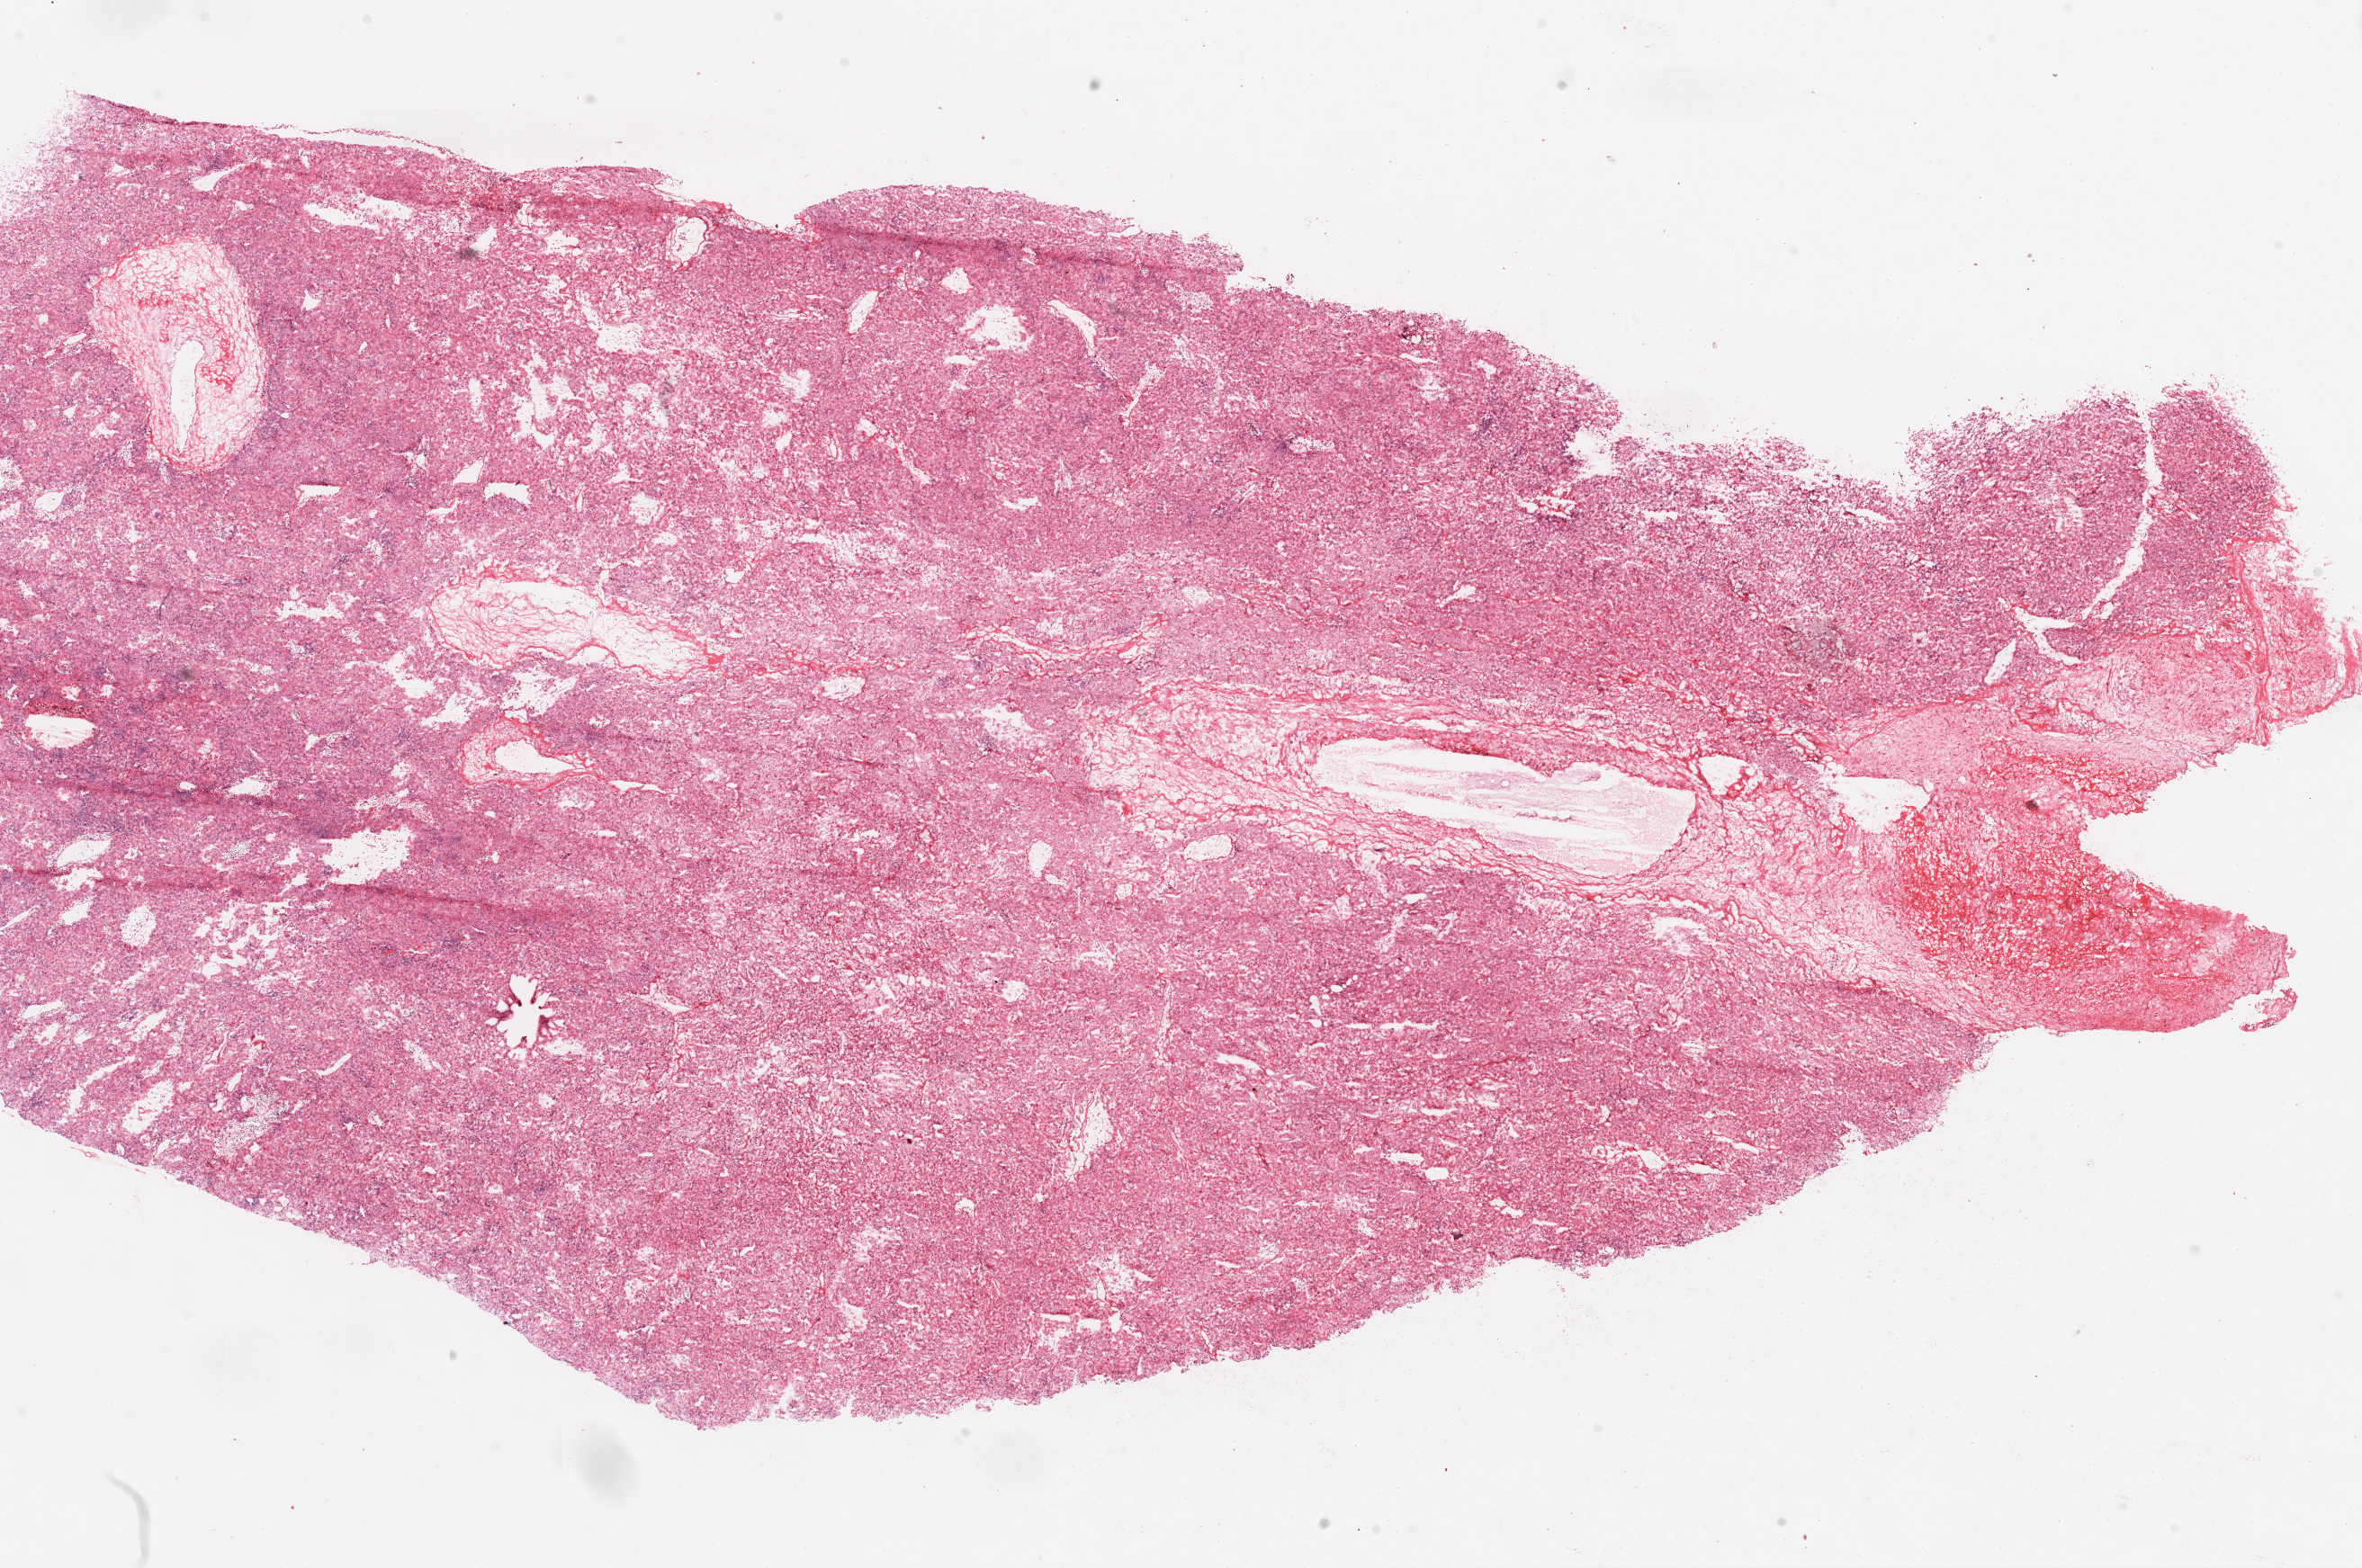
Digitized H&E tissue section (whole slide) — a low-resolution overview of the entire scanned area, about 21.1 x 14.0 mm, frozen section from the top of the tissue portion, sample: primary tumour, kidney. Male patient; age at initial diagnosis 69 years. Histologic grade: G2 (moderately differentiated). Pathologist review of this section (percent, as recorded): tumour cells 90%, tumour nuclei 85%, normal cells 0%, stromal cells 10%, necrosis 0%. Inflammatory infiltration, as recorded: lymphocyte infiltration 5%, monocyte infiltration 0%, neutrophil infiltration 0%.
* AJCC pathologic stage: II (6th edition)
* diagnosis: Clear cell adenocarcinoma, NOS
* lymph nodes positive (case pathology): 0 of 5 examined